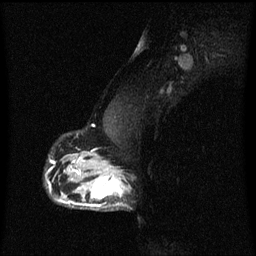
Breast MRI (dynamic contrast-enhanced), one sagittal slice; slice 42 of 60 in the series (ordered by position); dynamic contrast-enhanced series, image 2 of 3 at this slice position (ordered by acquisition); 1.5 T; TE 4.2 ms, TR 8.4 ms; 256 × 256 image matrix, field of view 200 × 200 mm. Patient: female, 40 years.
Annotated regions visible in this slice (semi-automatic segmentation, software-assisted and operator-edited):
- analysis volume of interest (the breast-tissue region the enhancement analysis was run in; not a lesion): bounding box <76,172,129,211> (left, top, right, bottom; pixels)
- tumour enhancement mask (voxels above the 70 % enhancement threshold inside the analysis volume of interest): <76,172,128,209>